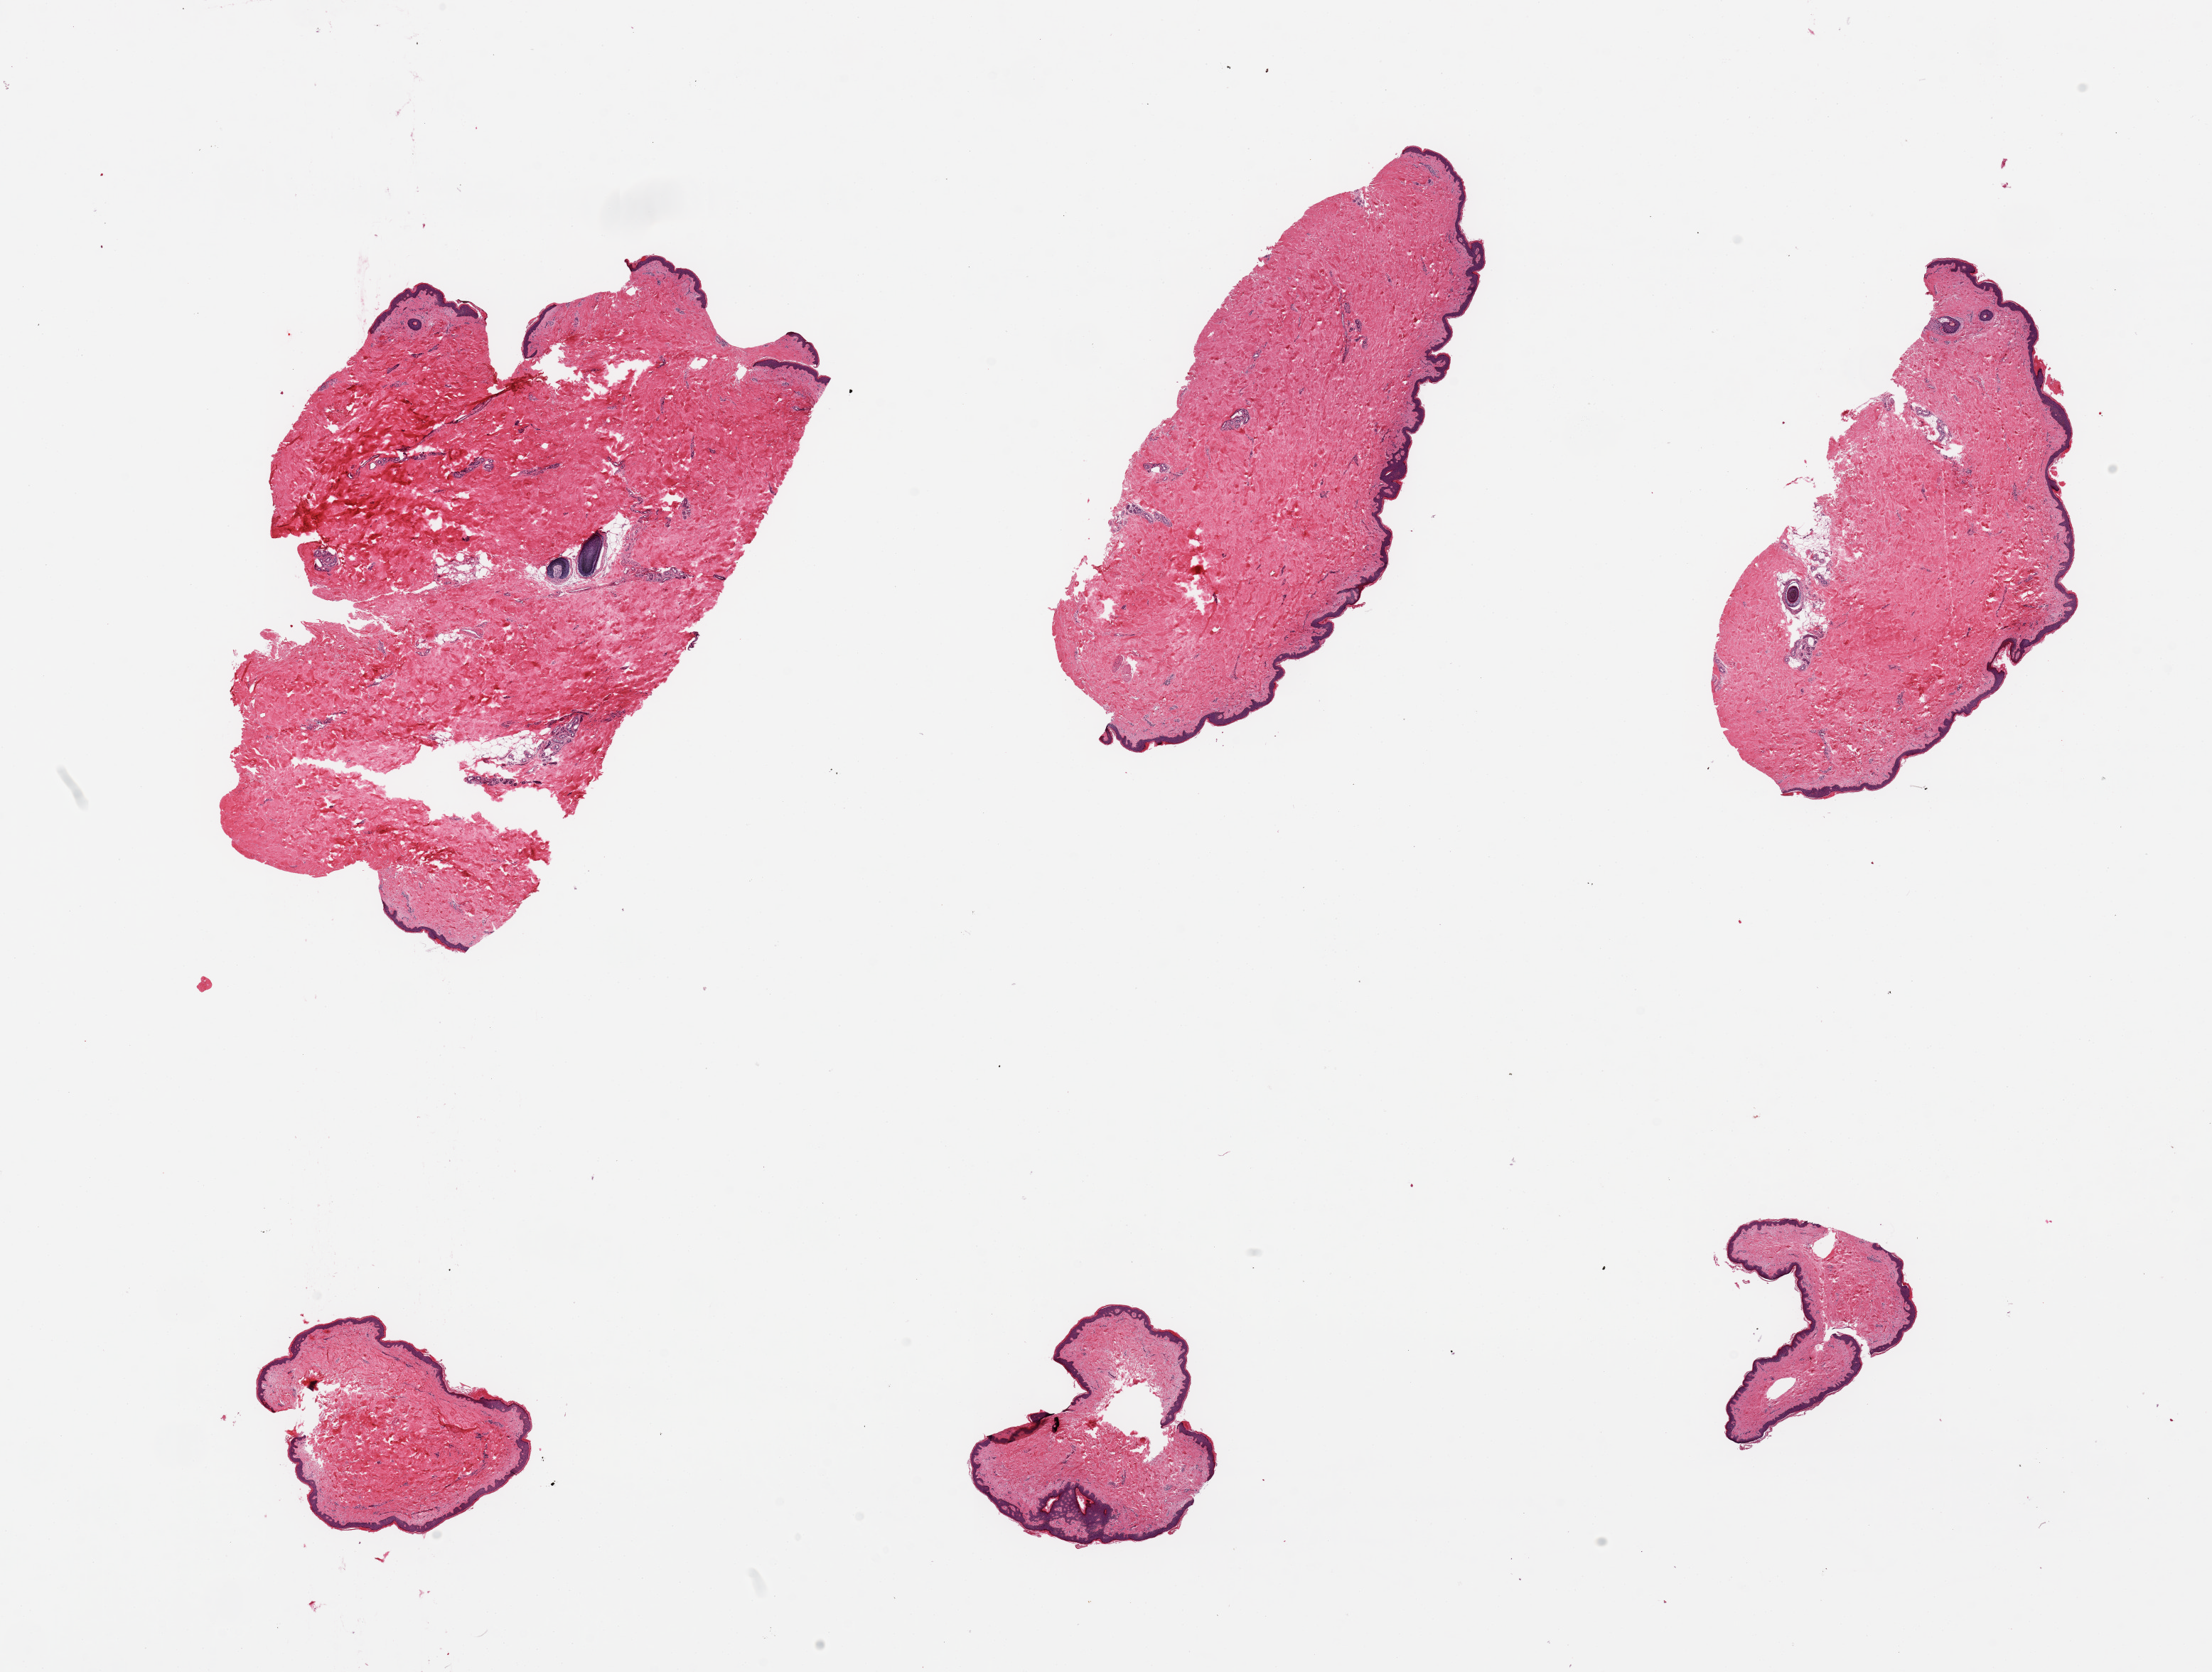
Digitized H&E-stained section, whole scanned area (about 24.6 x 18.6 mm) shown as a low-resolution overview, PAXgene-fixed, paraffin-embedded tissue, target tissue: skin of suprapubic region, tissue donor sample. Donor sex: male.
Review note (as recorded): 6 pieces, 3 large, 3 small; well trimmed; <5% dermal fat.